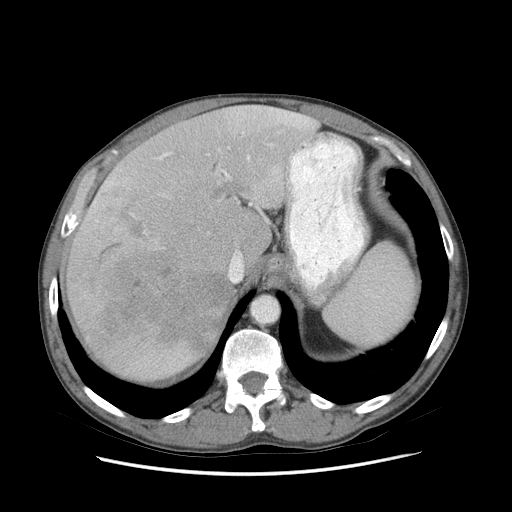
Contrast-enhanced abdominal CT (liver protocol), one axial slice. Position 59 of 89 along the scan axis. Reconstruction kernel STANDARD. 140 kVp. Soft-tissue window (W 400 / L 40 HU). 2.5 mm slice thickness. 512 × 512 image matrix. Case-level facts recorded for this patient, not image findings: diagnosis: hepatocellular carcinoma (patient treated with transarterial chemoembolisation; whether this scan precedes or follows treatment is not stated here); TNM stage (as recorded): Stage-IIIB; Child-Pugh class: A; tumour differentiation: moderately differentiated.
Annotated regions visible in this slice (semi-automatically segmented with operator editing):
- liver parenchyma outside the tumour (the mass and vessels are separate outlines, so this box may not span the whole liver): bounding box <66,104,316,380> (left, top, right, bottom; pixels)
- mass: <69,208,226,360>
- liver vessels: <93,107,310,283>